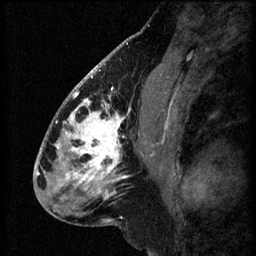
Breast MRI (dynamic contrast-enhanced), one sagittal slice; 3 images stored at this slice position (order not interpretable as contrast timing); 1.5 T; TE 4.2 ms, TR 8.2 ms; 256 × 256 image matrix, field of view 180 × 180 mm. Patient: female, 41 years.
Annotated regions visible in this slice (semi-automatically segmented with operator editing):
- analysis volume of interest (the breast-tissue region the enhancement analysis was run in; not a lesion): bounding box <56,104,157,207> (left, top, right, bottom; pixels)
- tumour enhancement mask (voxels above the 70 % enhancement threshold inside the analysis volume of interest): <56,104,153,199>